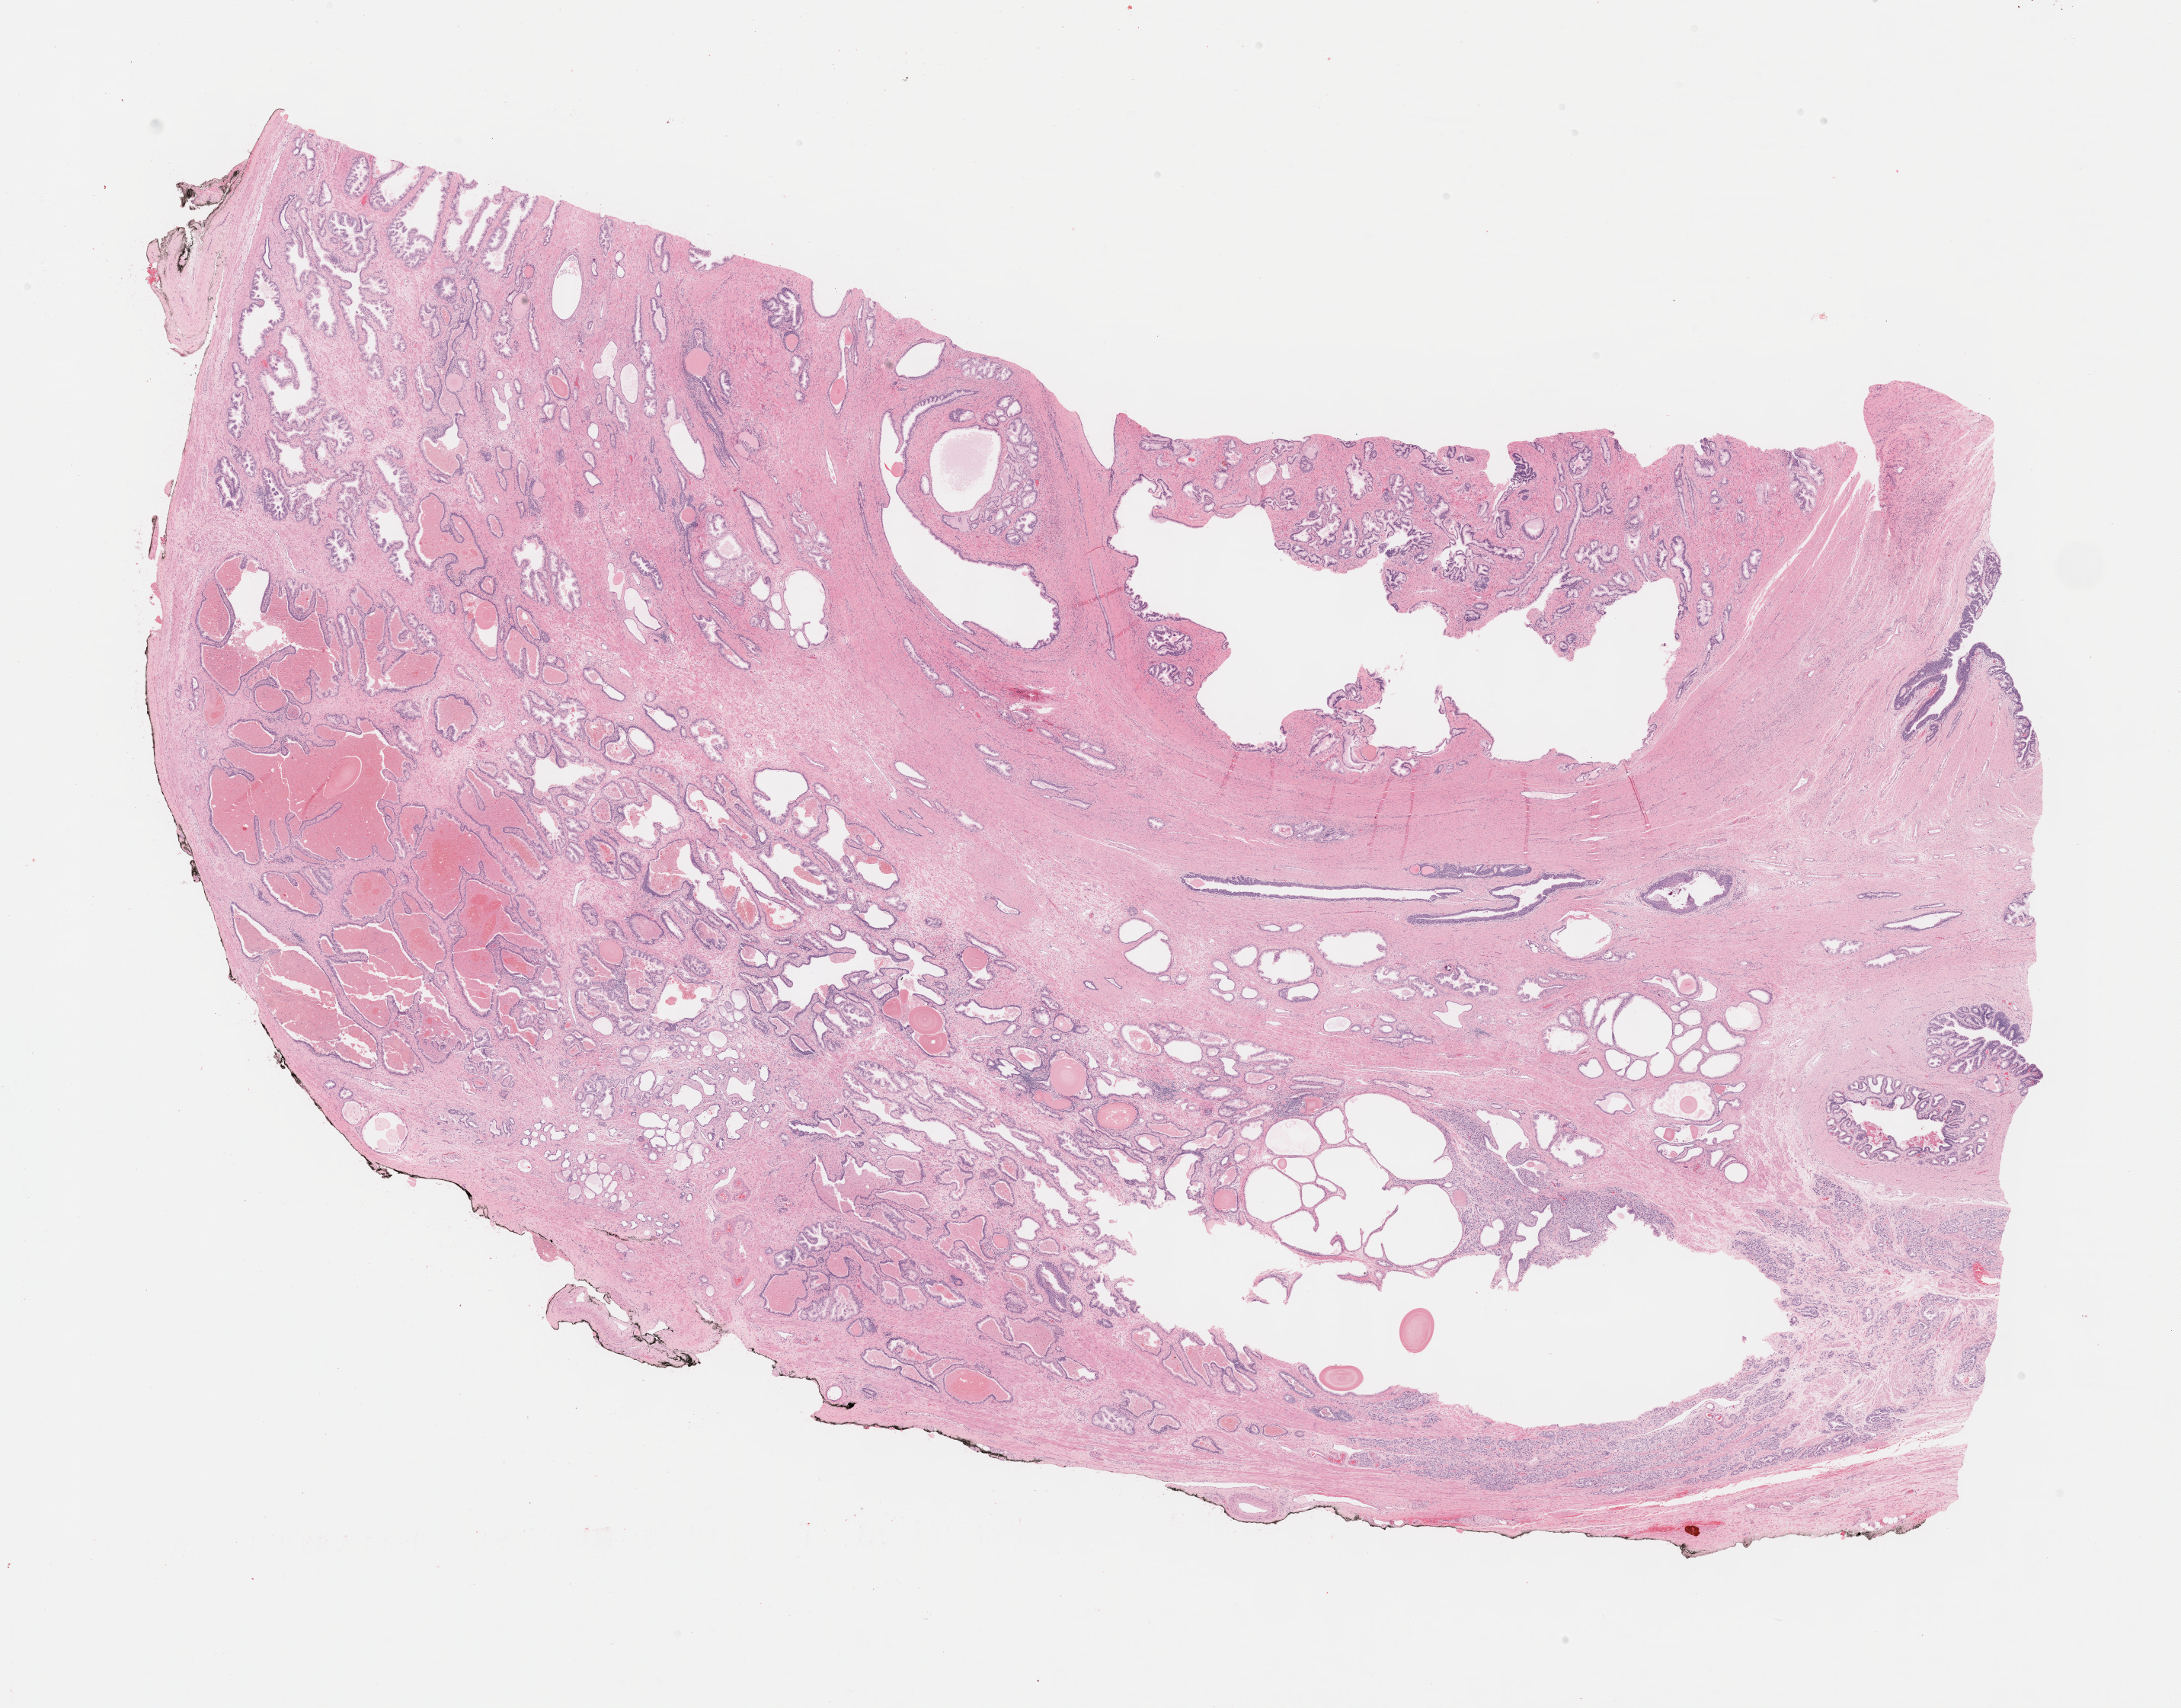
Digitized H&E tissue section (whole slide) — a low-resolution overview of the entire scanned area, about 23.2 x 18.1 mm; FFPE section; prostate, primary tumour sample. Male, age 56 years at initial diagnosis.
Diagnosis: Adenocarcinoma, NOS (prostate gland).